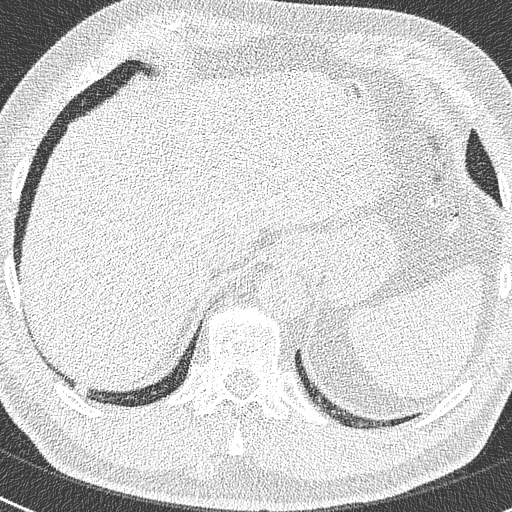
Chest CT (low-dose screening protocol), one axial image. Second annual screen. Lung window (W 1500 / L -600 HU). Male, age 63 years at enrolment. Former smoker at enrolment.
Expert reader's lesion annotation, bounding box [x1, y1, x2, y2] px = [66, 376, 98, 403]. Screening reader's record for this exam: no non-calcified nodule ≥4 mm recorded. Later outcome: lung cancer diagnosed 262 days after this screen — adenocarcinoma, NOS, right lower lobe, moderately differentiated (G2), stage IIIB (AJCC 6th edition), 17 mm at pathology.